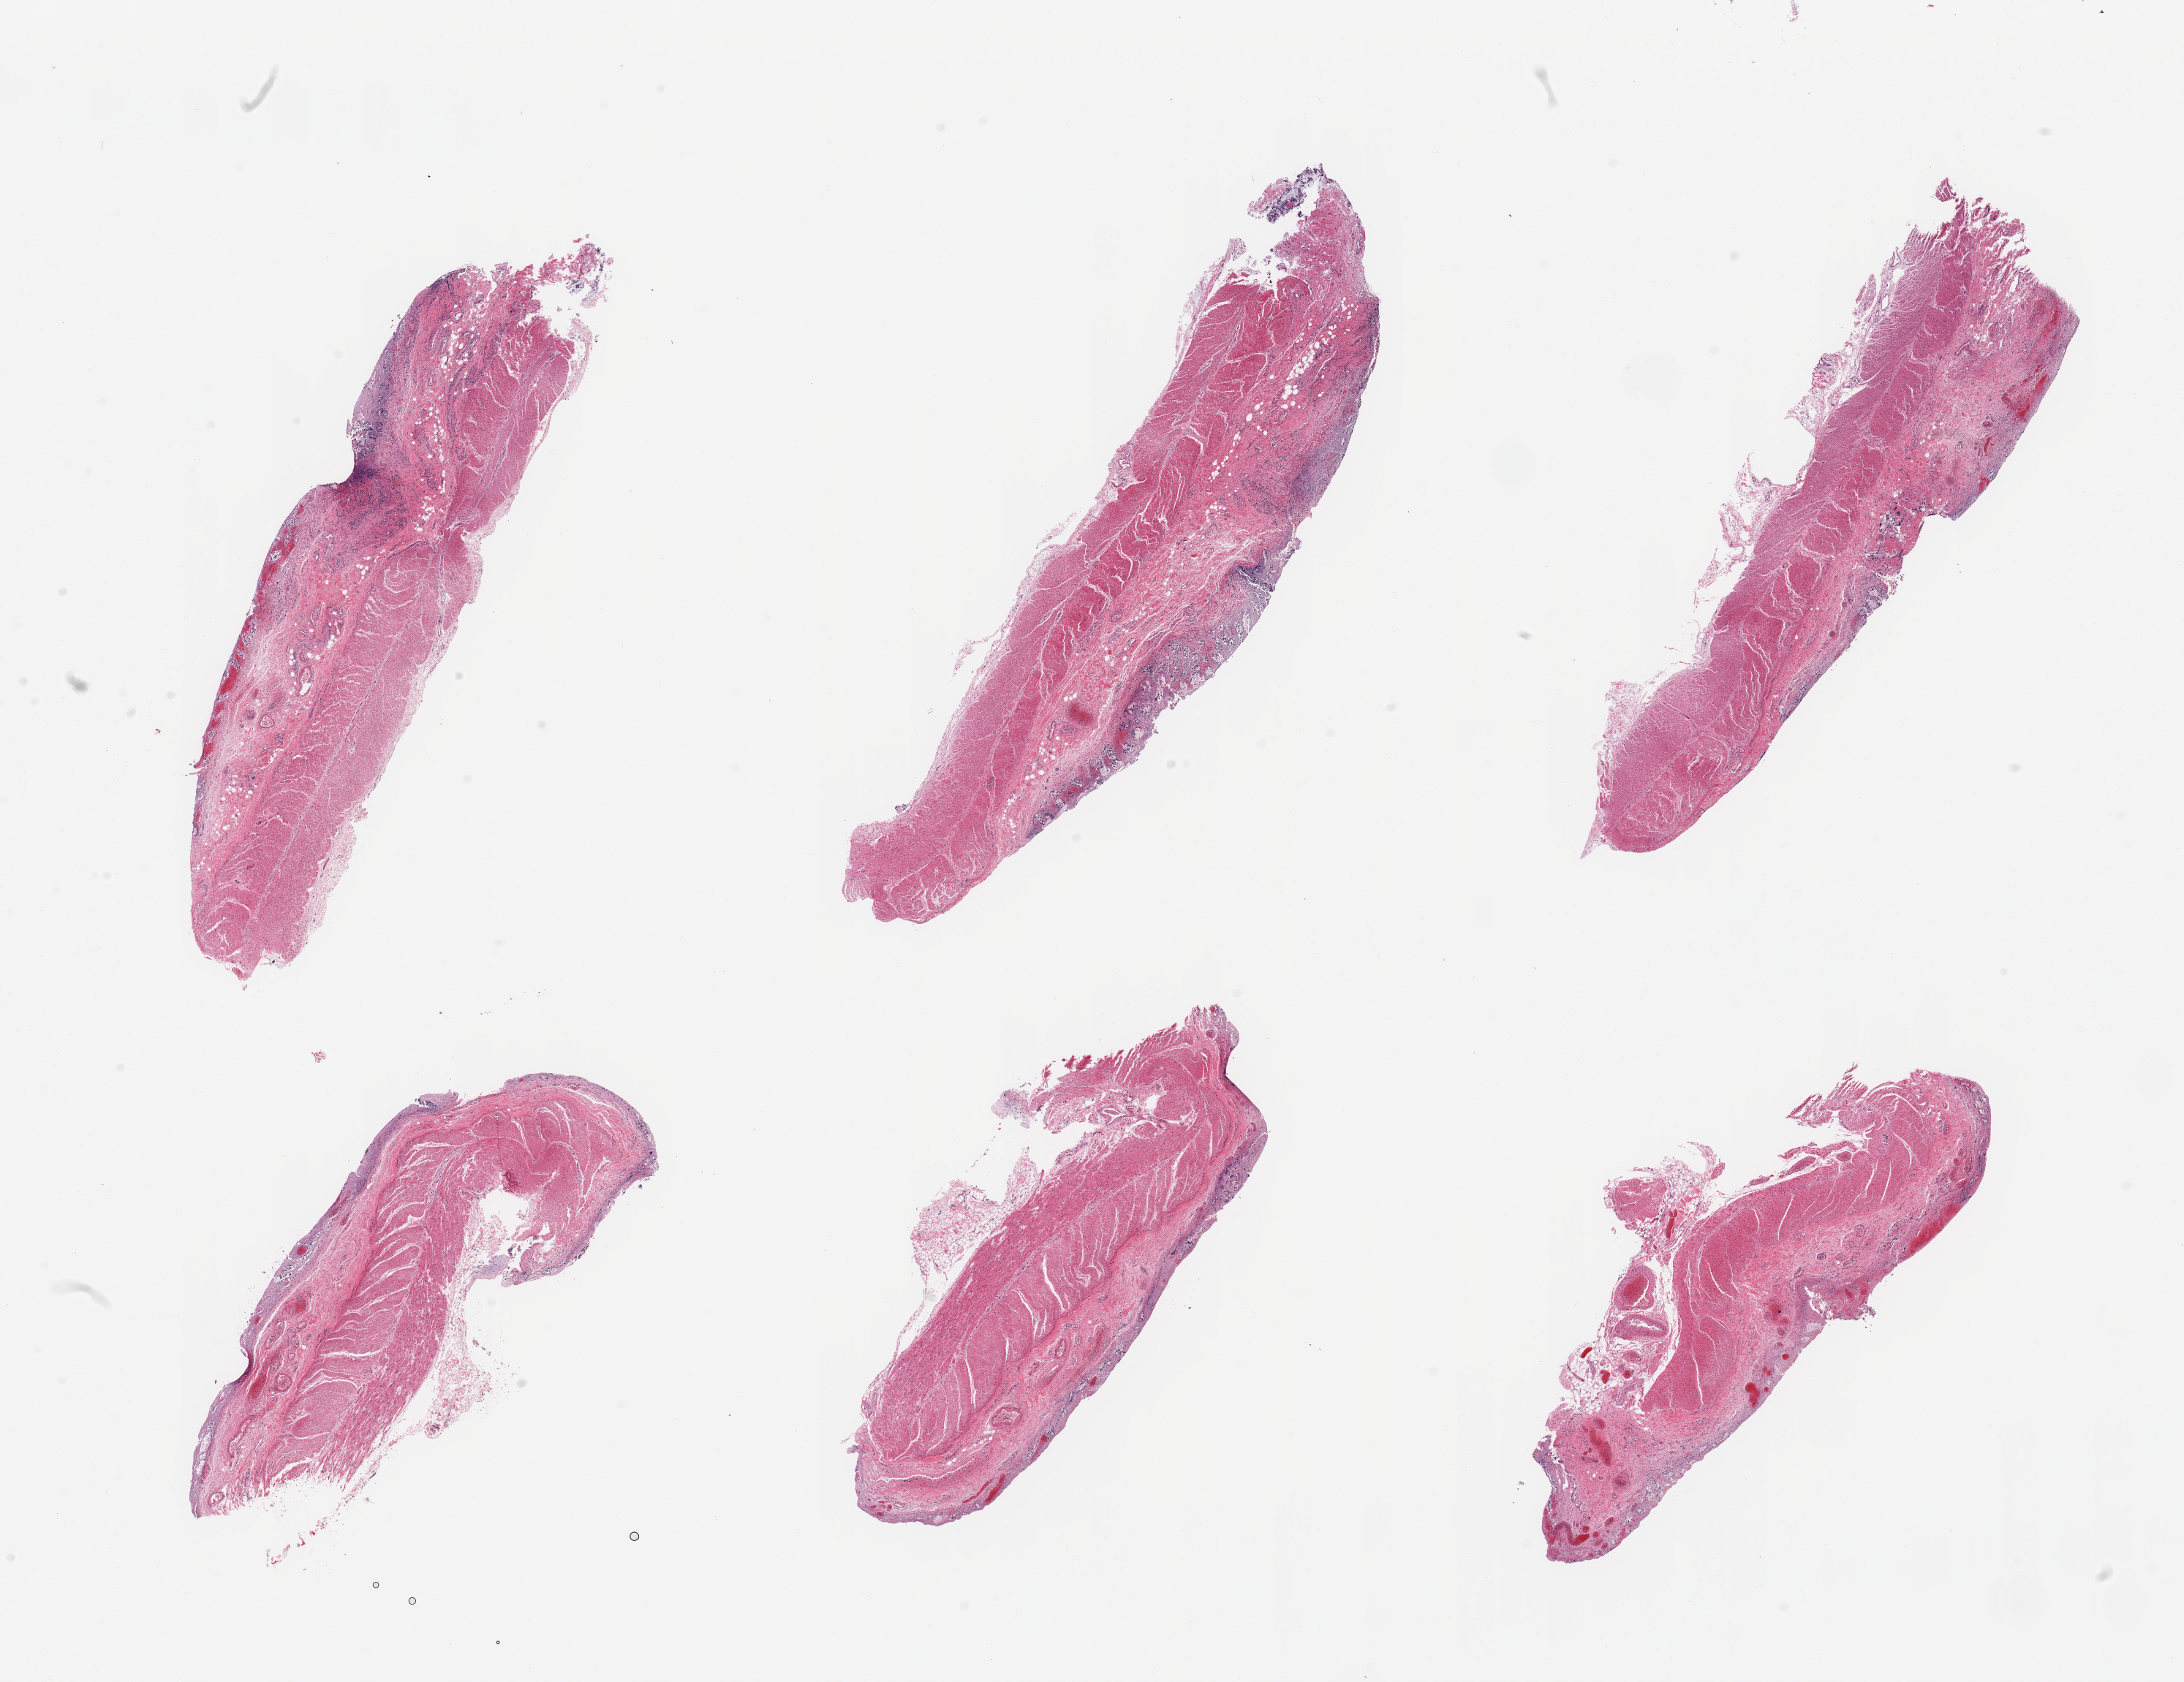
Digitized haematoxylin and eosin-stained section — a low-resolution overview of the entire scanned area, about 23.6 x 18.2 mm (acquisition: 20x scan), PAXgene-fixed paraffin-embedded (PFPE) section, section of transverse colon (target tissue), donor tissue sample. Female donor.
Pathologist's review note for this sample: 6 pieces, mucosa with advanced autolysis, largely sloughed.